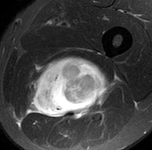
MRI of an extremity soft-tissue mass, one axial slice; slice 76 of 90 in the series (ordered by position); STIR; MR volume resampled by the dataset authors to the PET/CT grid (not the native acquisition matrix); 3.27 mm slice thickness; 152 × 150 image matrix. Male patient. From the clinical record (not read from this slice): histological type: undifferentiated pleomorphic liposarcoma; grade: high; site of the primary tumour: left thigh.
Annotated regions visible in this slice (expert contour drawn on MRI and transferred to this co-registered scan by the dataset authors):
- gross tumour volume including surrounding oedema: bounding box (x1, y1, x2, y2) in pixels: (25, 55, 115, 124)
- gross tumour volume (mass): (34, 57, 113, 117)